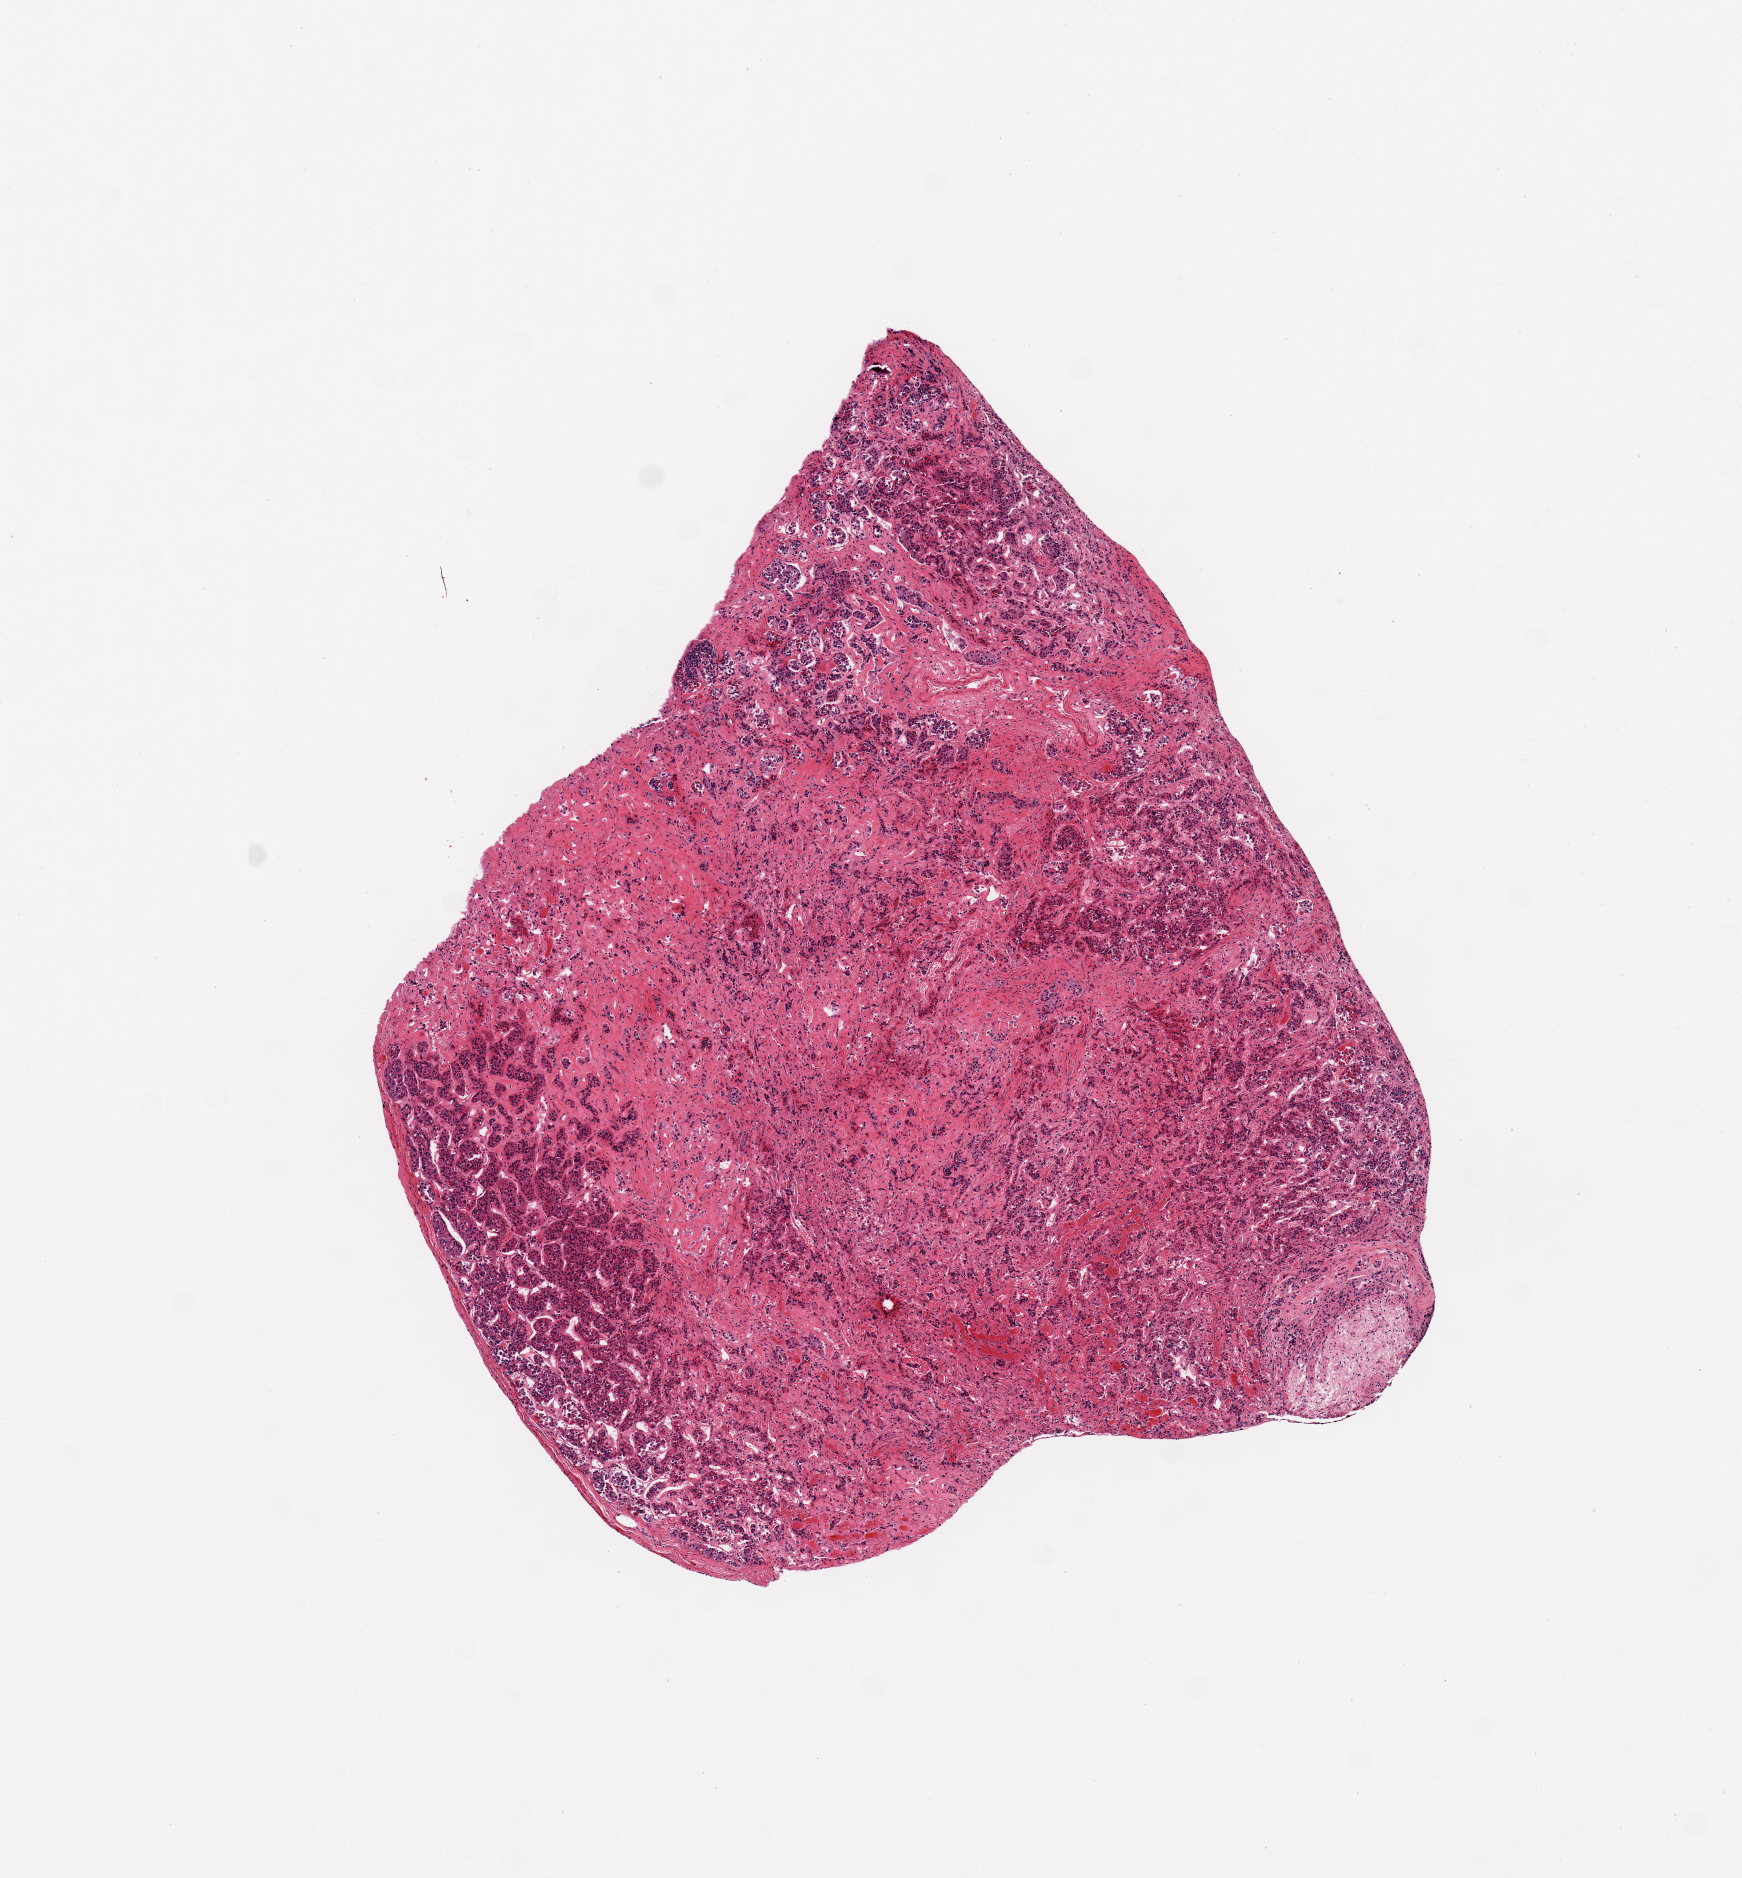
Whole-slide image, haematoxylin and eosin stain — low-resolution overview of the scanned area, about 6.9 x 7.4 mm. PAXgene-fixed paraffin-embedded (PFPE) section. Sampled site (target tissue): pituitary. Donor tissue sample.
Reviewer comment on this tissue sample: 1 piece; predominantly adenohypophysis and tiny focus of neurohypohysis.